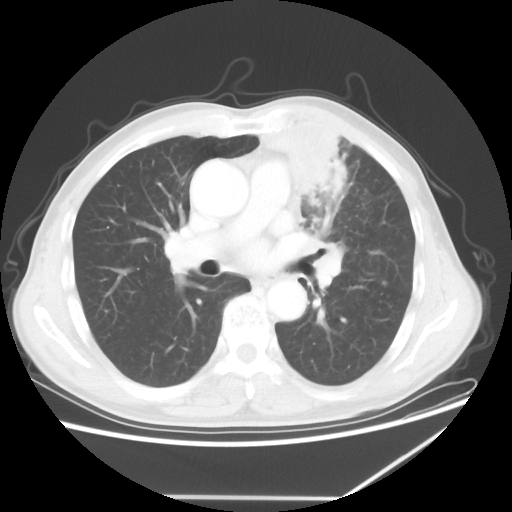
Chest CT, one axial slice. Slice 35 of 64 in the series (ordered by position). Reconstruction kernel STANDARD. 100 kVp. Lung window (W 1500 / L -600 HU). 512 × 512 image matrix, field of view 383 × 383 mm. Patient: male, 64 years. Case-level facts recorded for this patient, not image findings: clinical TNM (as recorded): T1c N1 M1; histopathological grade: G2.
Outlined on this slice (bounding box drawn by a radiologist):
- lung tumour (recorded histology: squamous cell carcinoma): bounding box [x1, y1, x2, y2] px = [261, 117, 359, 233]